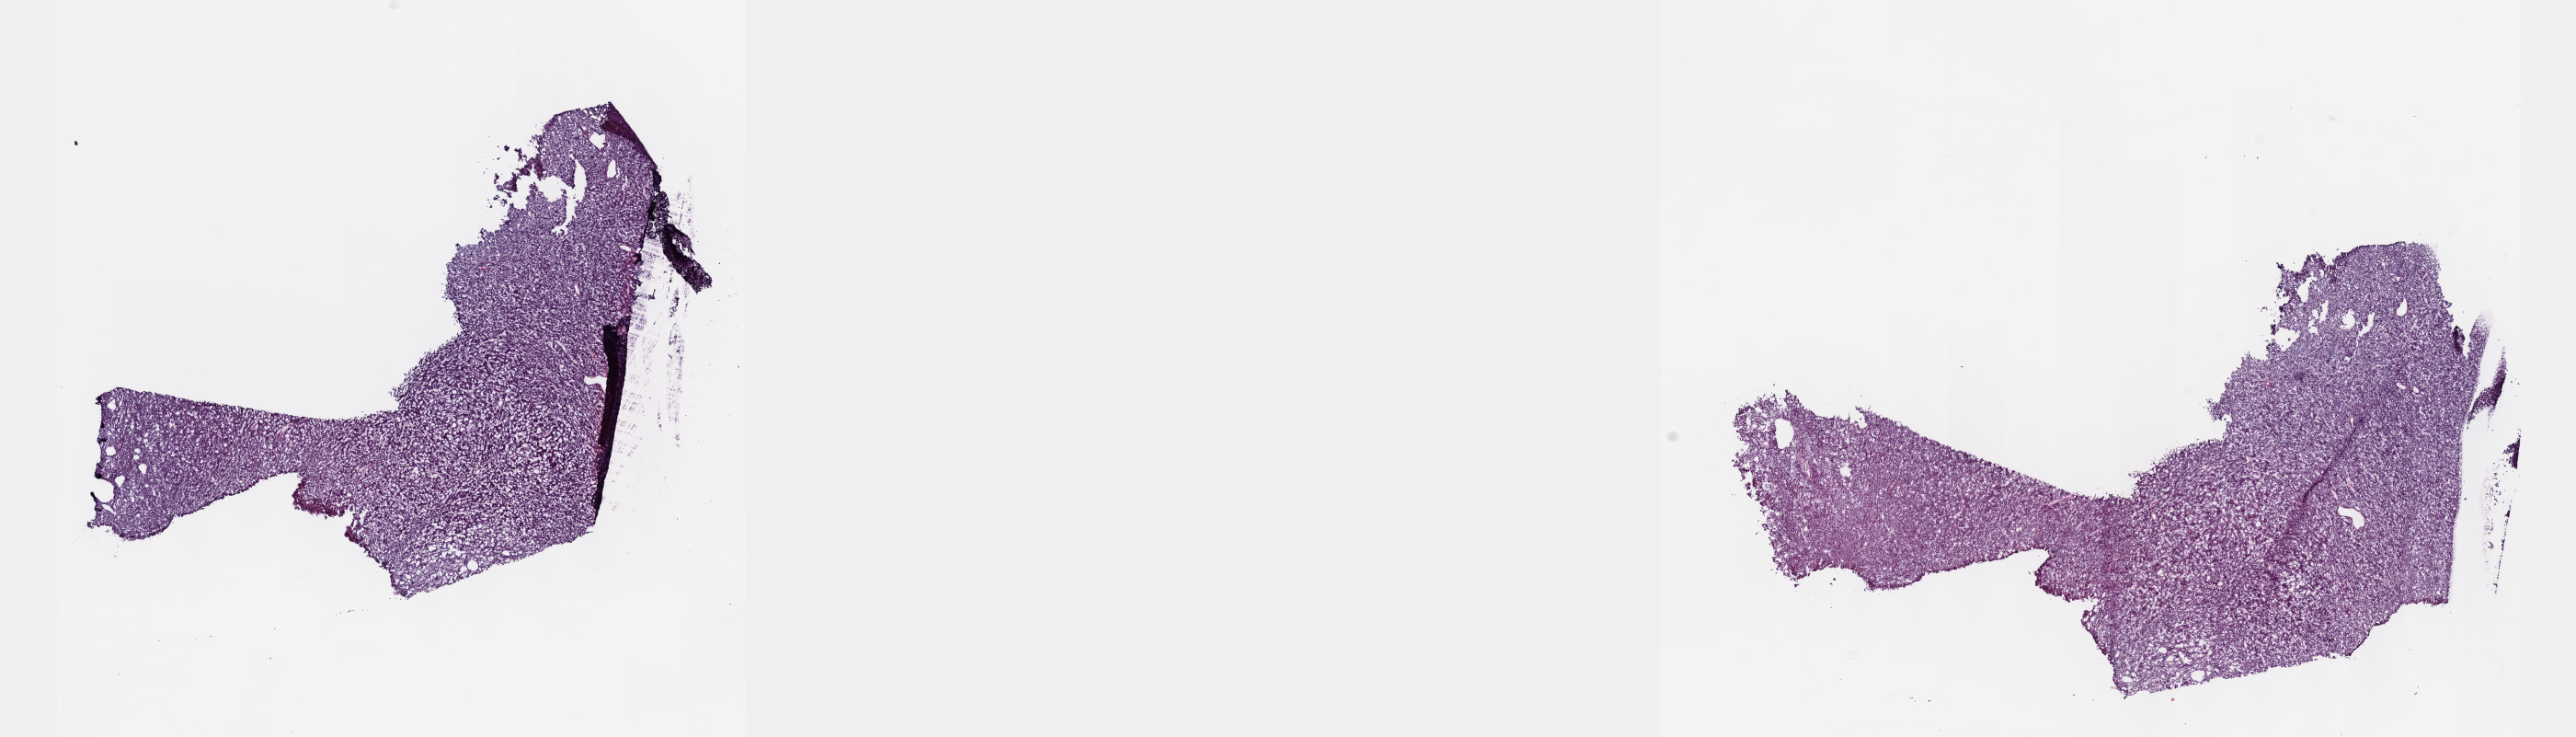
Whole-slide histology image, H&E-stained, shown as a low-resolution overview of the whole scanned area (about 22.6 x 6.5 mm, slide scanned at 40x), frozen section from the top of the tissue portion, primary tumour sample from the kidney. Patient sex: male. Composition of this section per pathologist review: tumour cells 90%, tumour nuclei 95%, normal cells 0%, stromal cells 10%, necrosis 0%. Infiltration values recorded for this section: lymphocyte infiltration 0%, monocyte infiltration 0%, neutrophil infiltration 0%.
AJCC pathologic stage: I (6th edition). Pathologic diagnosis: Papillary adenocarcinoma, NOS.